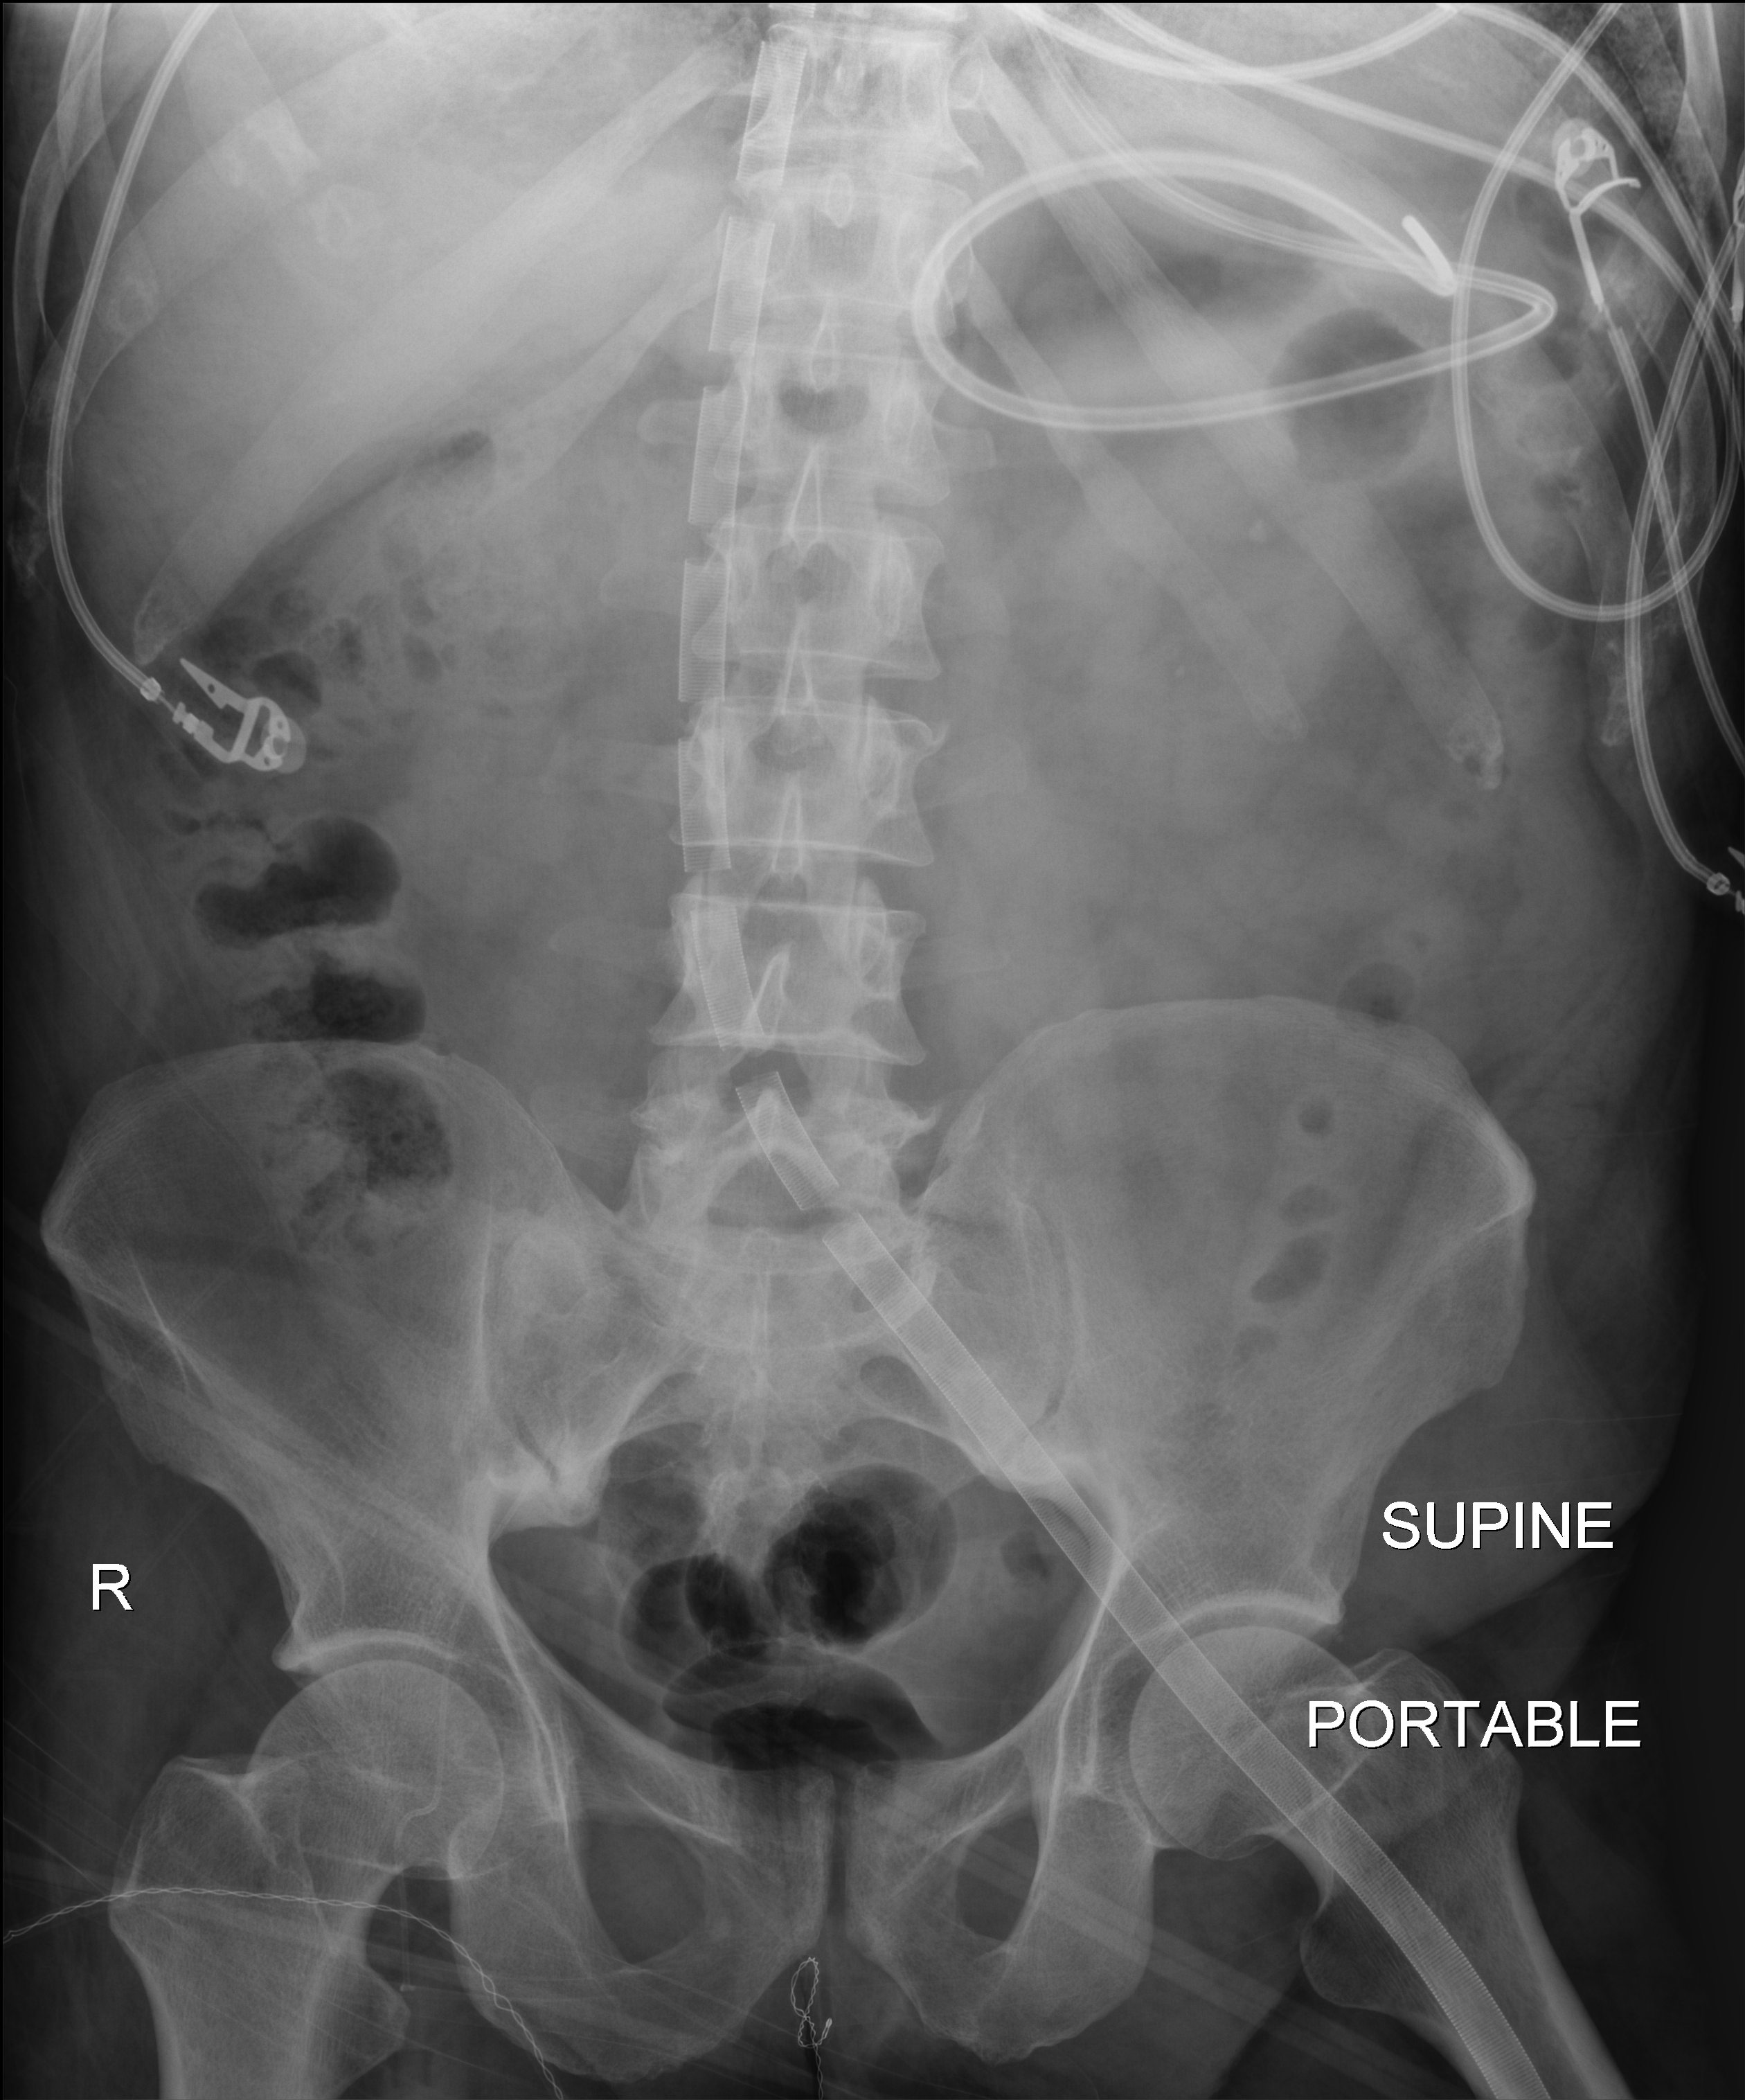
Abdomen radiograph, anteroposterior (AP) projection. Patient hospitalised with COVID-19; male, aged 18–59 years.
Hospital-stay facts (about this admission, not read from this image; timing relative to this image not recorded): admitted to intensive care during this hospital stay: yes; other chronic lung disease (admission record): no; mechanically ventilated during this hospital stay: yes.